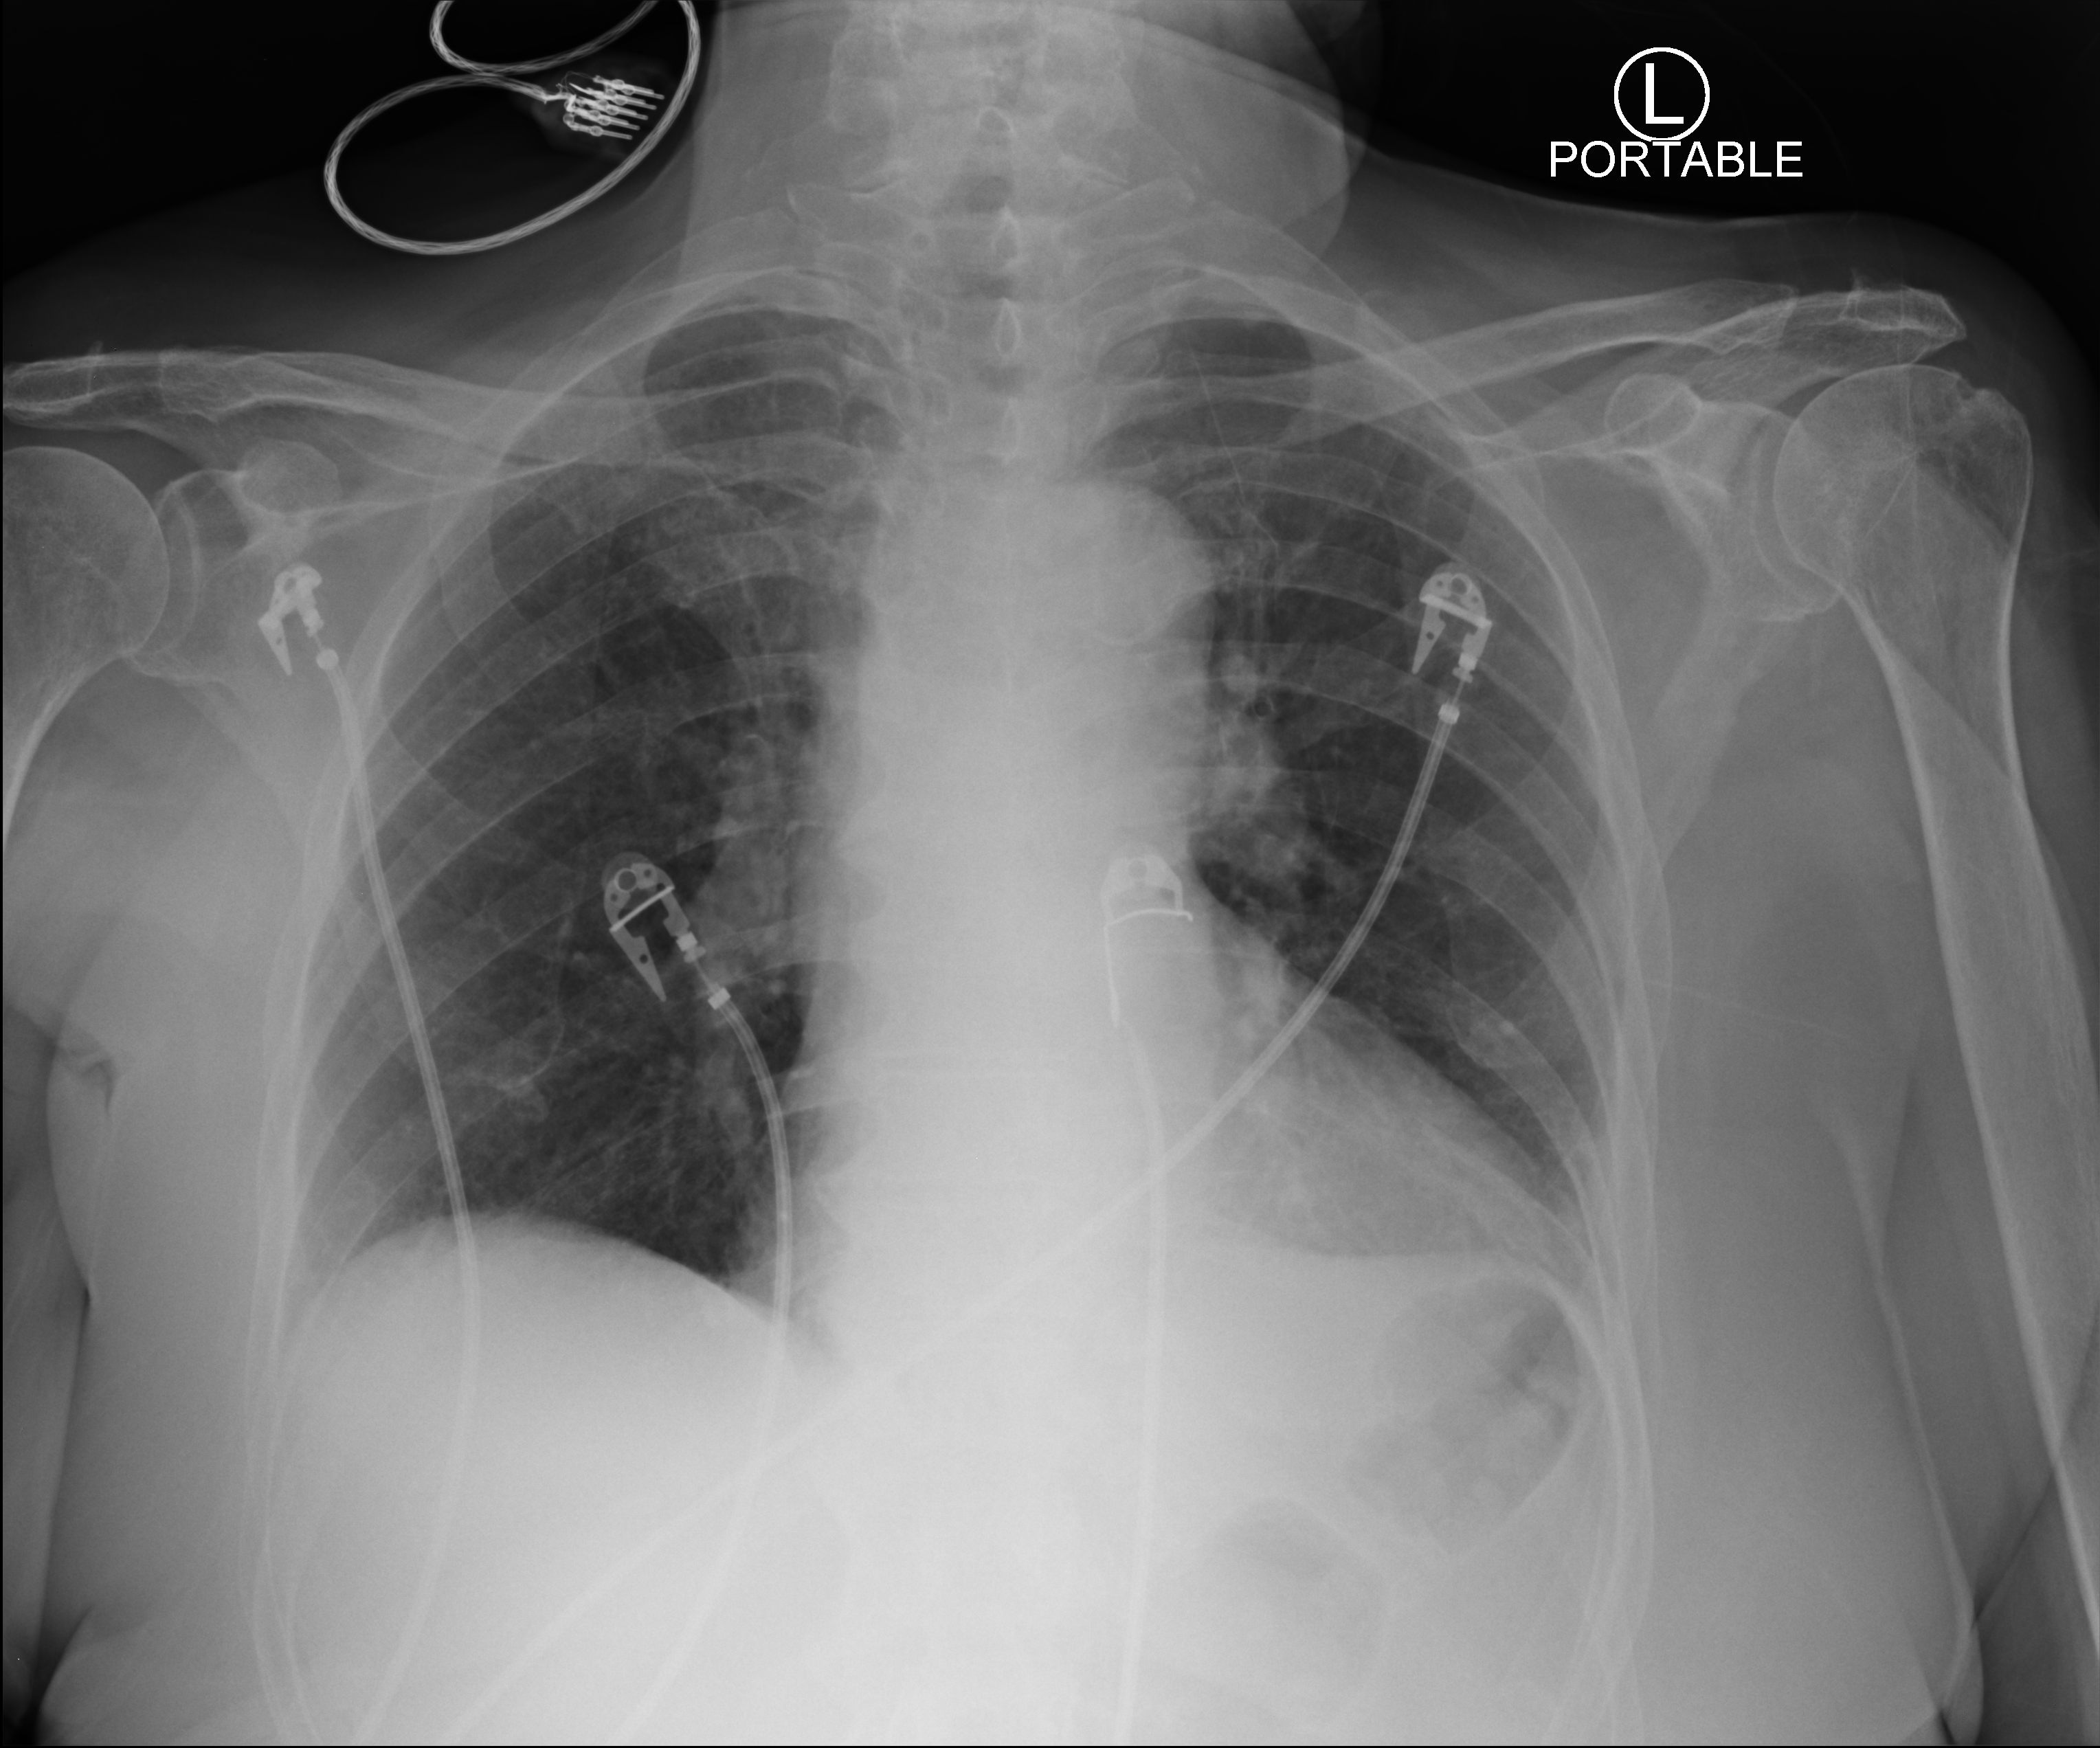
Portable chest radiograph. Patient hospitalised with COVID-19; female, aged 75–90 years.
Admission-level facts for this patient (not findings on this image; timing relative to this image not recorded): other chronic lung disease (admission record): no; admitted to intensive care during this hospital stay: no.